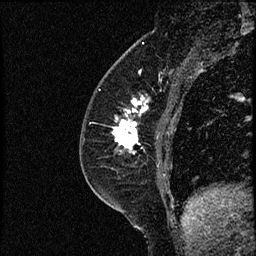
Breast MRI (dynamic contrast-enhanced), one sagittal slice. Slice 24 of 52 in the series (ordered by position). Dynamic contrast-enhanced study with each time point stored as its own series, time point 2 of 3 at this slice position (early post-contrast, ordered by acquisition time). 1.5 T. TE 4.2 ms, TR 17.6 ms. 2 mm slice thickness. 256 × 256 image matrix, field of view 200 × 200 mm. Female patient, age 49 years. Case-level facts recorded for this patient, not image findings: setting: breast cancer imaged before/during neoadjuvant chemotherapy; receptor status: HER2-positive.
Annotated regions visible in this slice (semi-automatic segmentation, software-assisted and operator-edited):
- analysis volume of interest (the breast-tissue region the enhancement analysis was run in; not a lesion): bounding box <85,65,182,175> (left, top, right, bottom; pixels)
- tumour enhancement mask (voxels above the 100 % enhancement threshold inside the analysis volume of interest): <111,98,148,155>